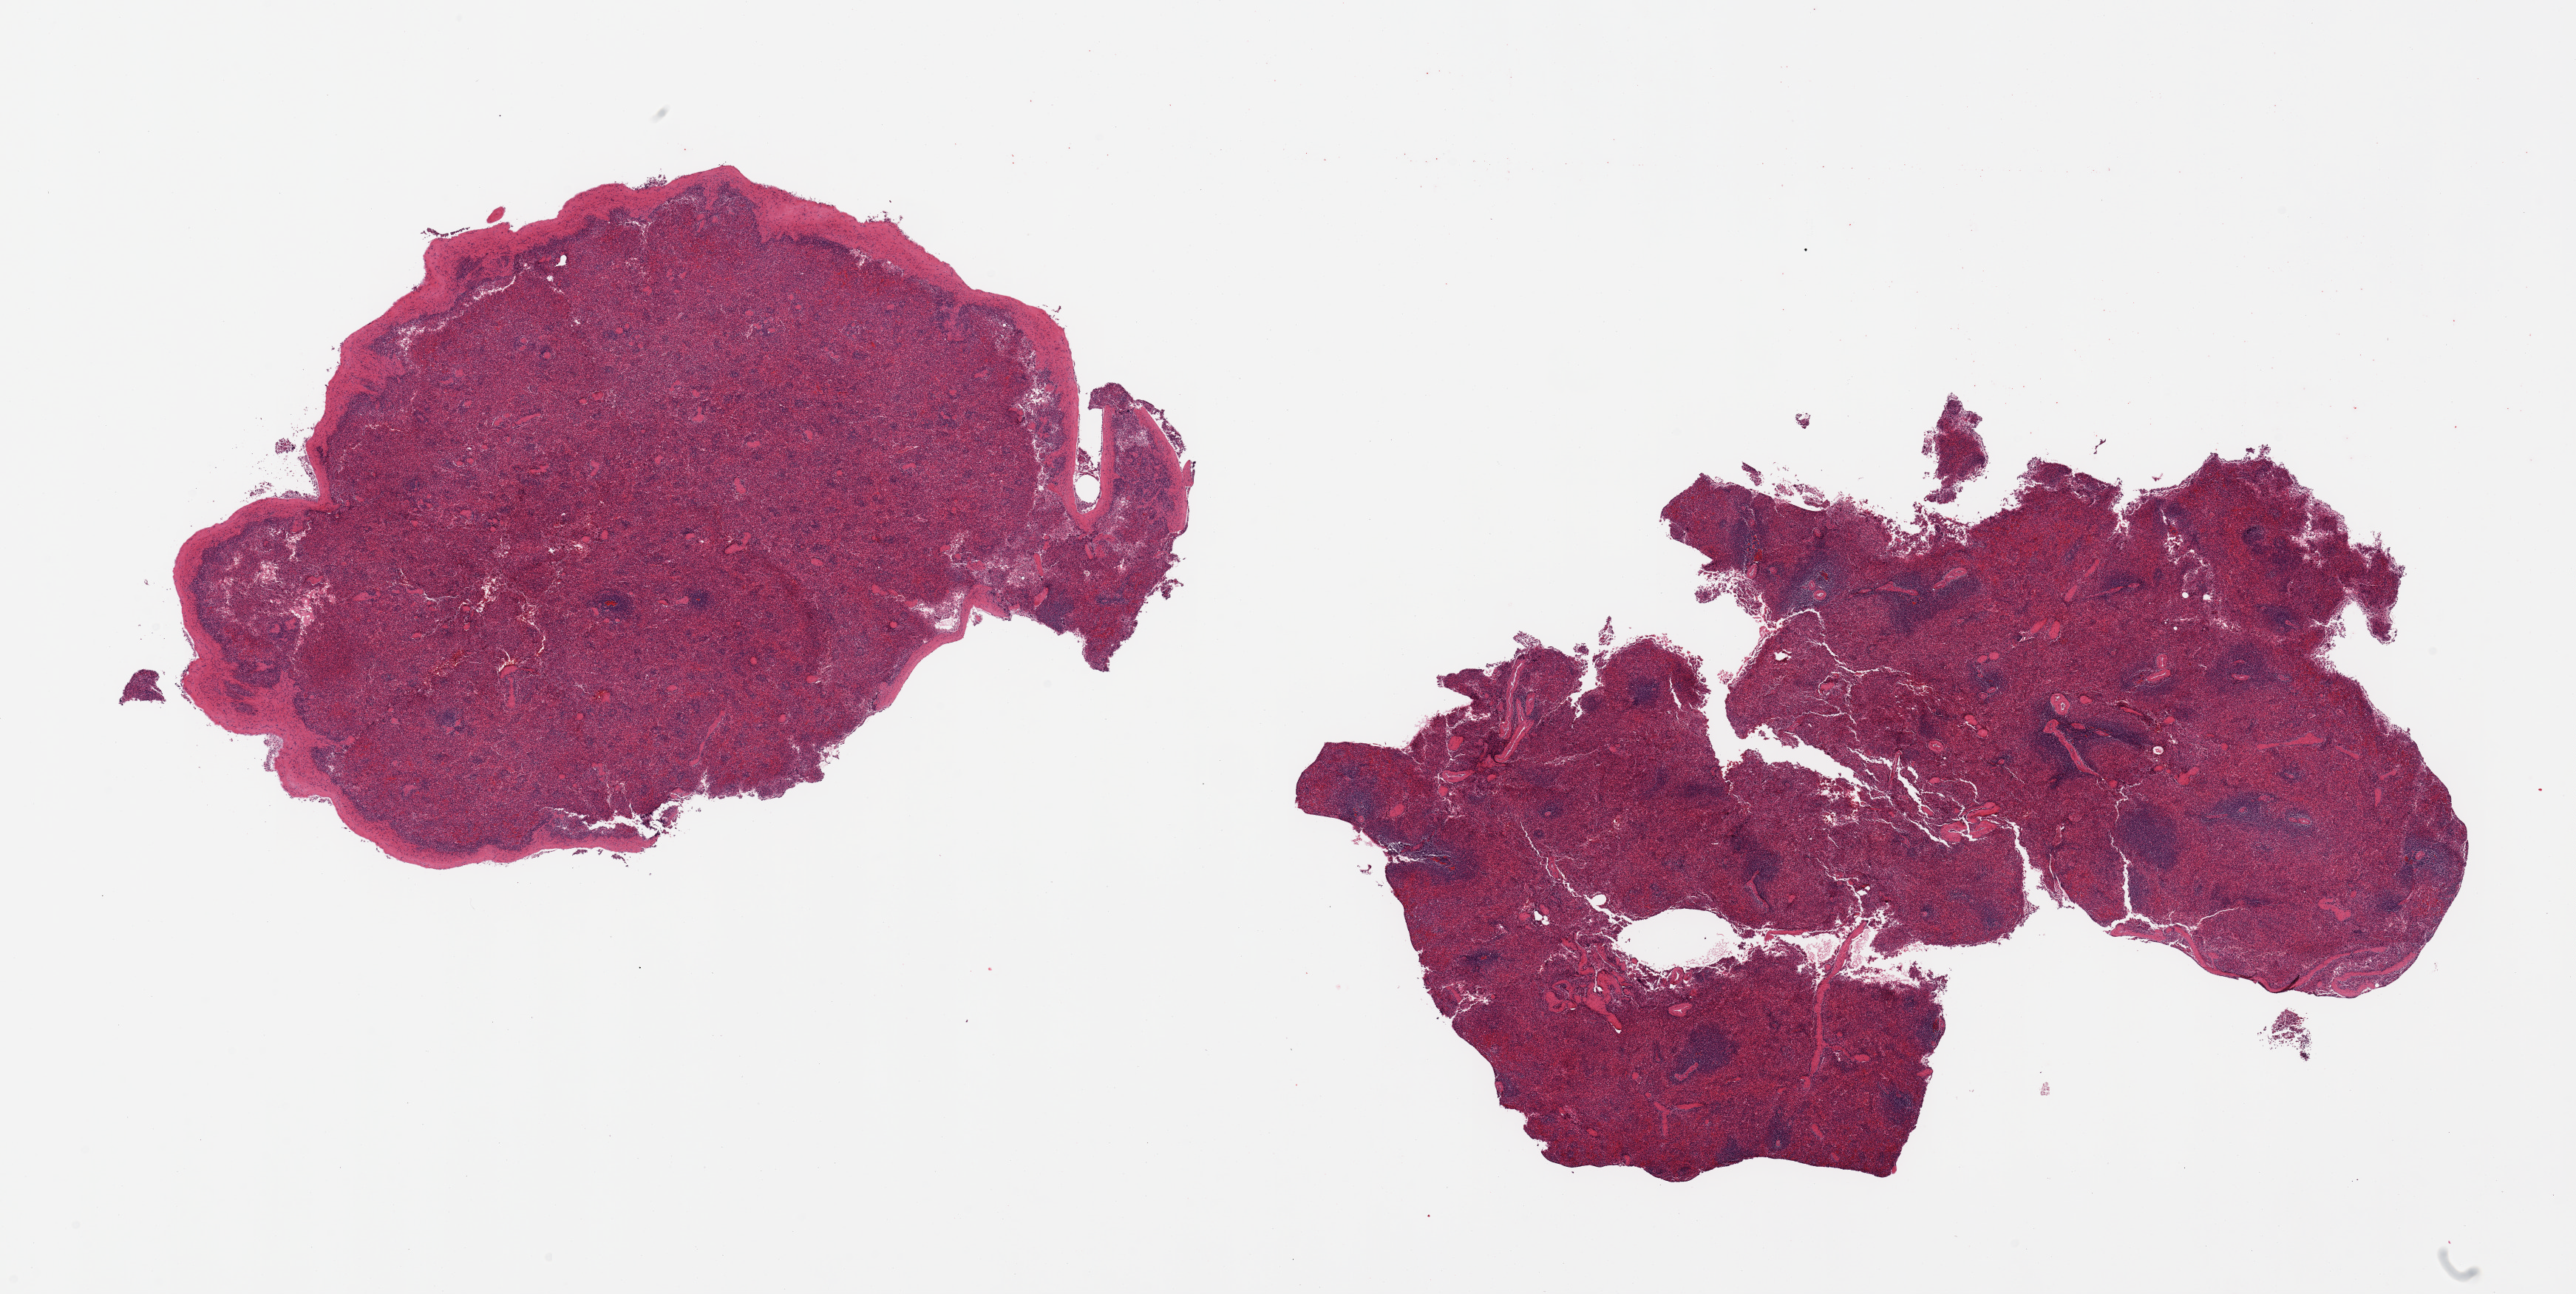
Digitized haematoxylin and eosin-stained section, brightfield, shown as a low-resolution overview of the whole scanned area (about 27.6 x 13.8 mm). PAXgene-fixed, paraffin-embedded tissue. Sampled site (target tissue): spleen. Donor tissue sample. Female donor.
Pathologist's review note for this sample: 2 pieces; congestion, one piece contains capsule.